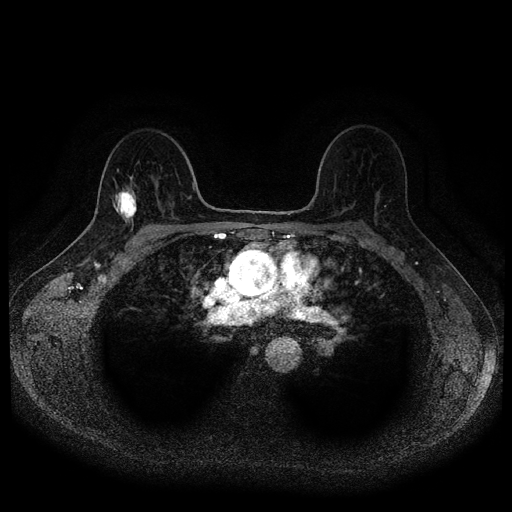
Breast MRI (dynamic contrast-enhanced, multi-phase), one axial slice; position 67 of 116 along the scan axis; dynamic contrast-enhanced series, time point 2 of 5 at this slice position (early post-contrast); 1.5 T; TE 2.6 ms, TR 5.4 ms; 2 mm slice thickness; 512 × 512 image matrix, field of view 340 × 340 mm. Patient: female, 49 years.
Annotated regions visible in this slice (semi-automatically segmented with operator editing):
- breast lesion (labelled 'tumour' in the annotation; benign lesions carry a separate 'benign' label): box from (x=113, y=188) to (x=137, y=221) px